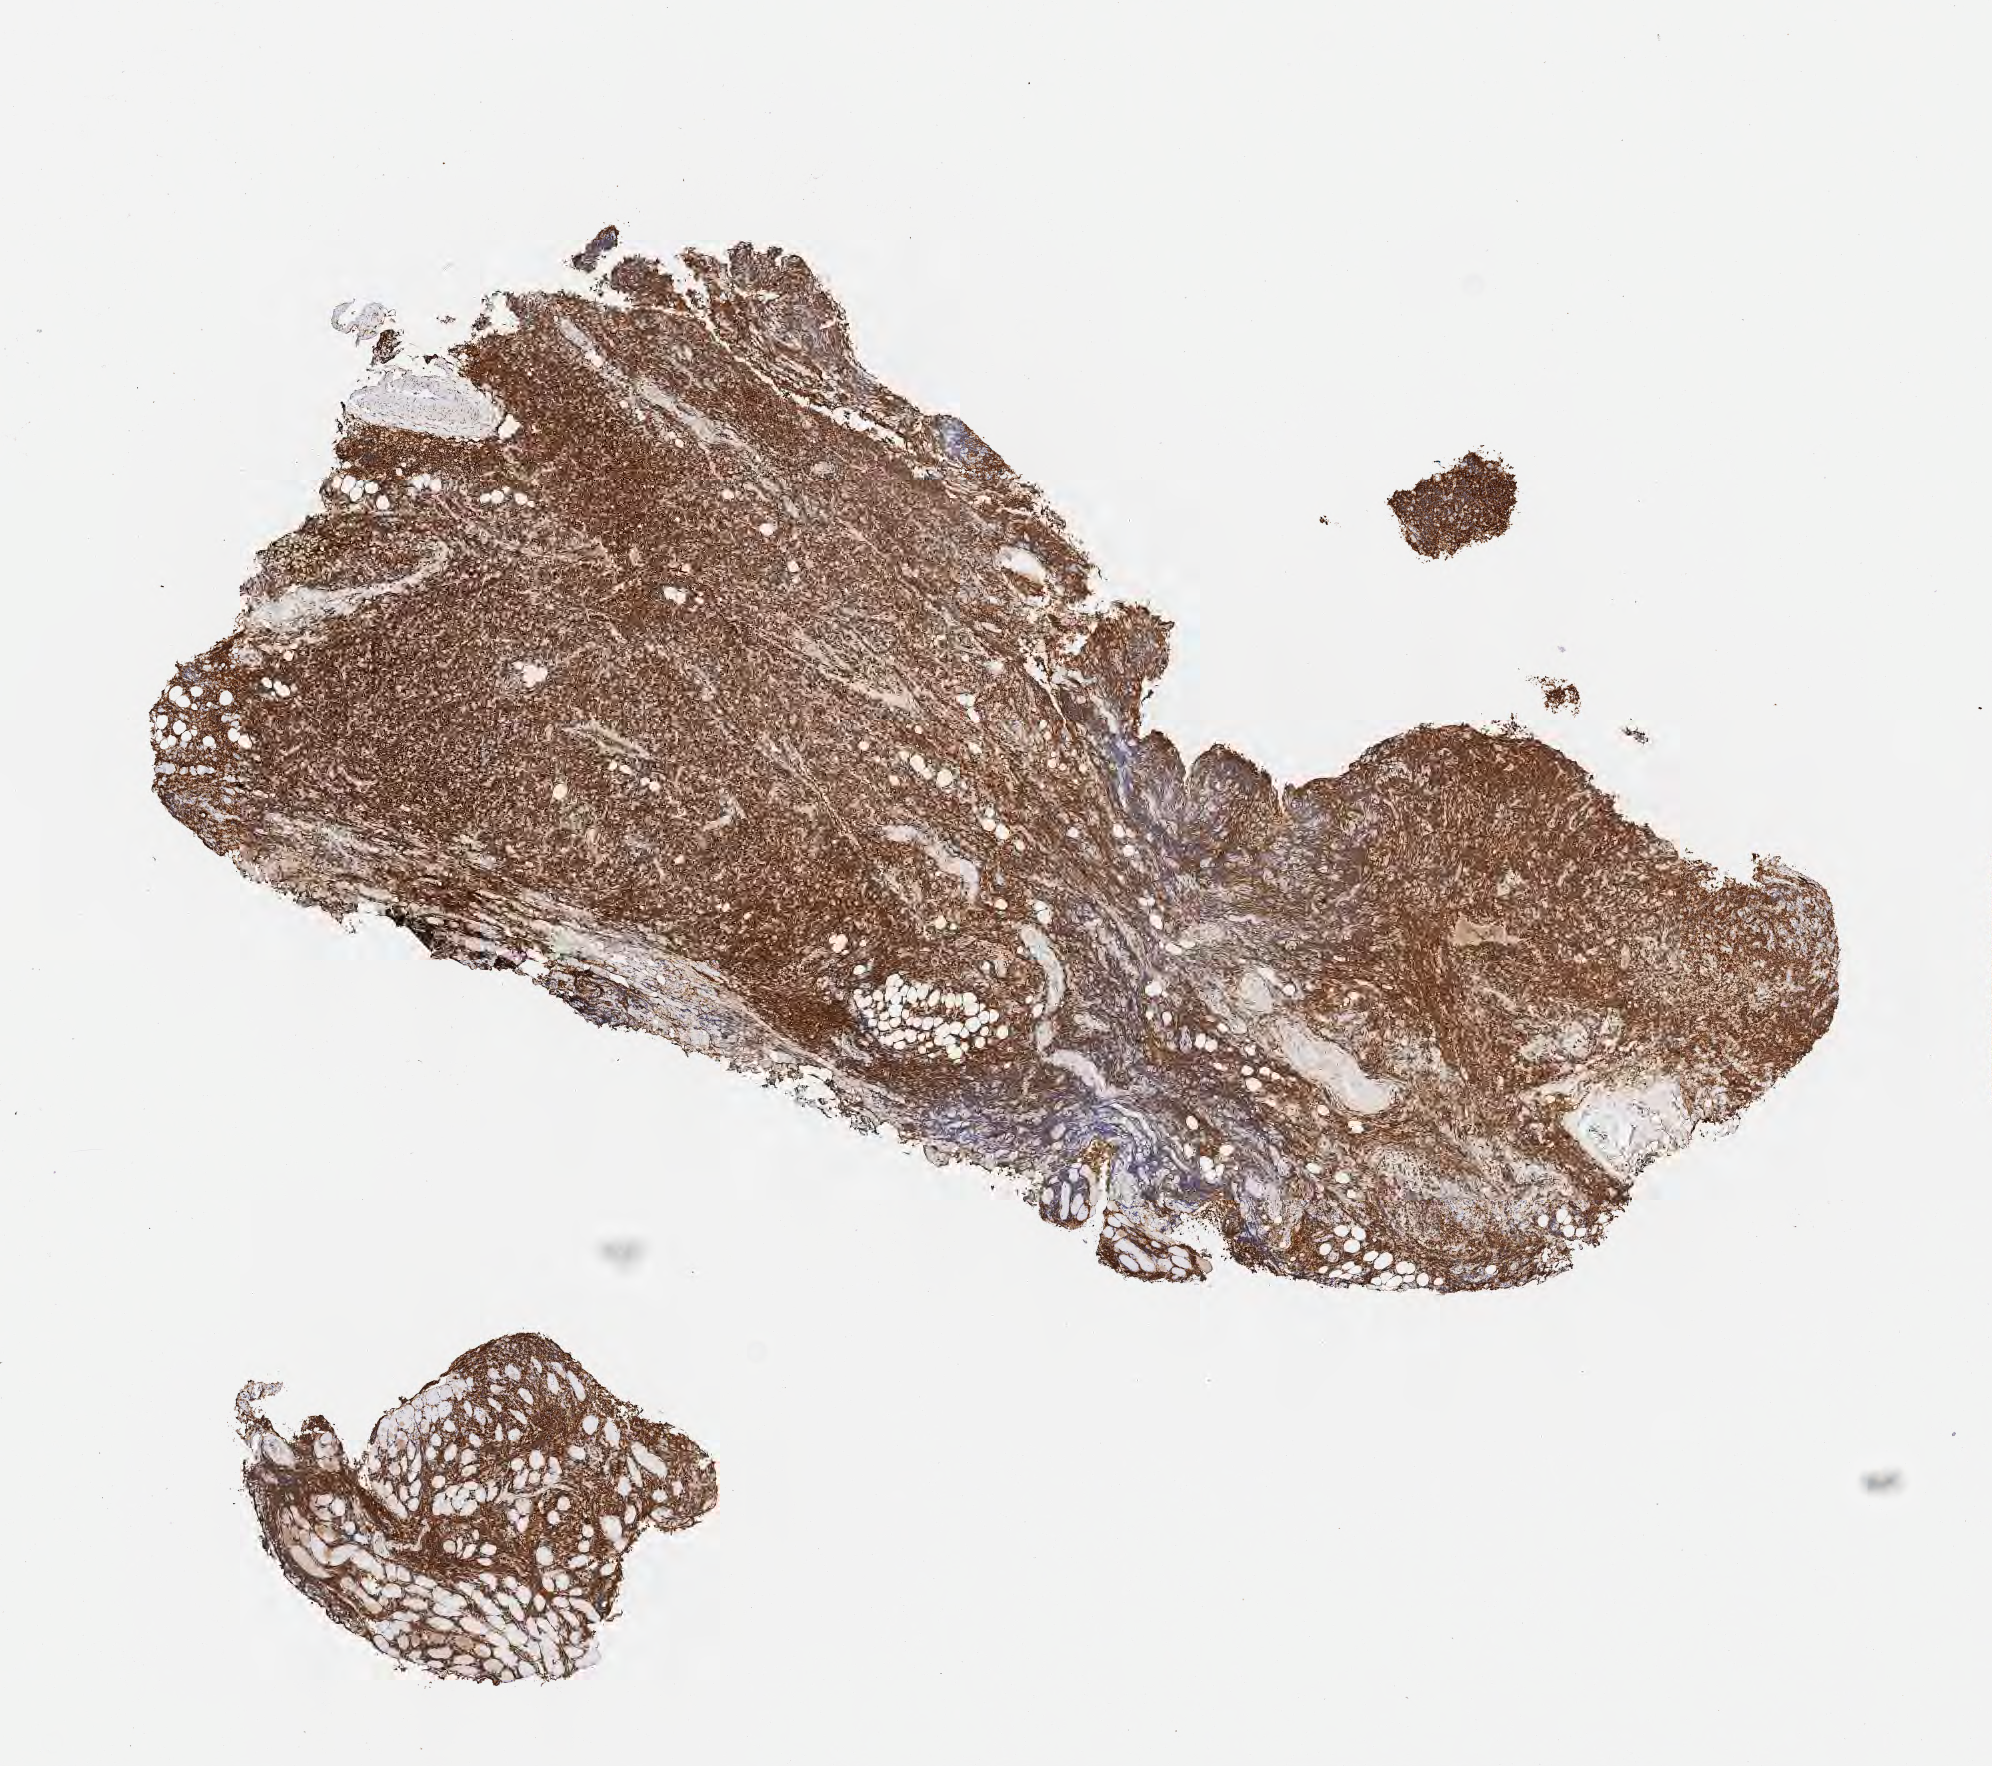
Immunohistochemistry (IHC) whole-slide image stained for BCL2, a low-resolution overview of the entire scanned area, about 8.0 x 7.1 mm, tumor tissue. Patient: male, 67 years old.
Histologic diagnosis: Diffuse large B-cell lymphoma, NOS.